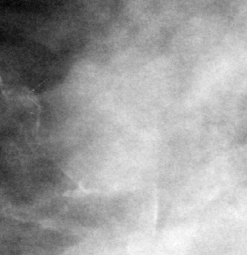
Region of interest cut from a scanned film mammogram (one marked finding); right breast; MLO view; BI-RADS breast density category 3 (scale 1–4).
- Mass, shape irregular, margins obscured / ill defined; BI-RADS assessment category 3; subtlety rating 2 on a 1 (subtle) to 5 (obvious) scale; pathology (as recorded): malignant.